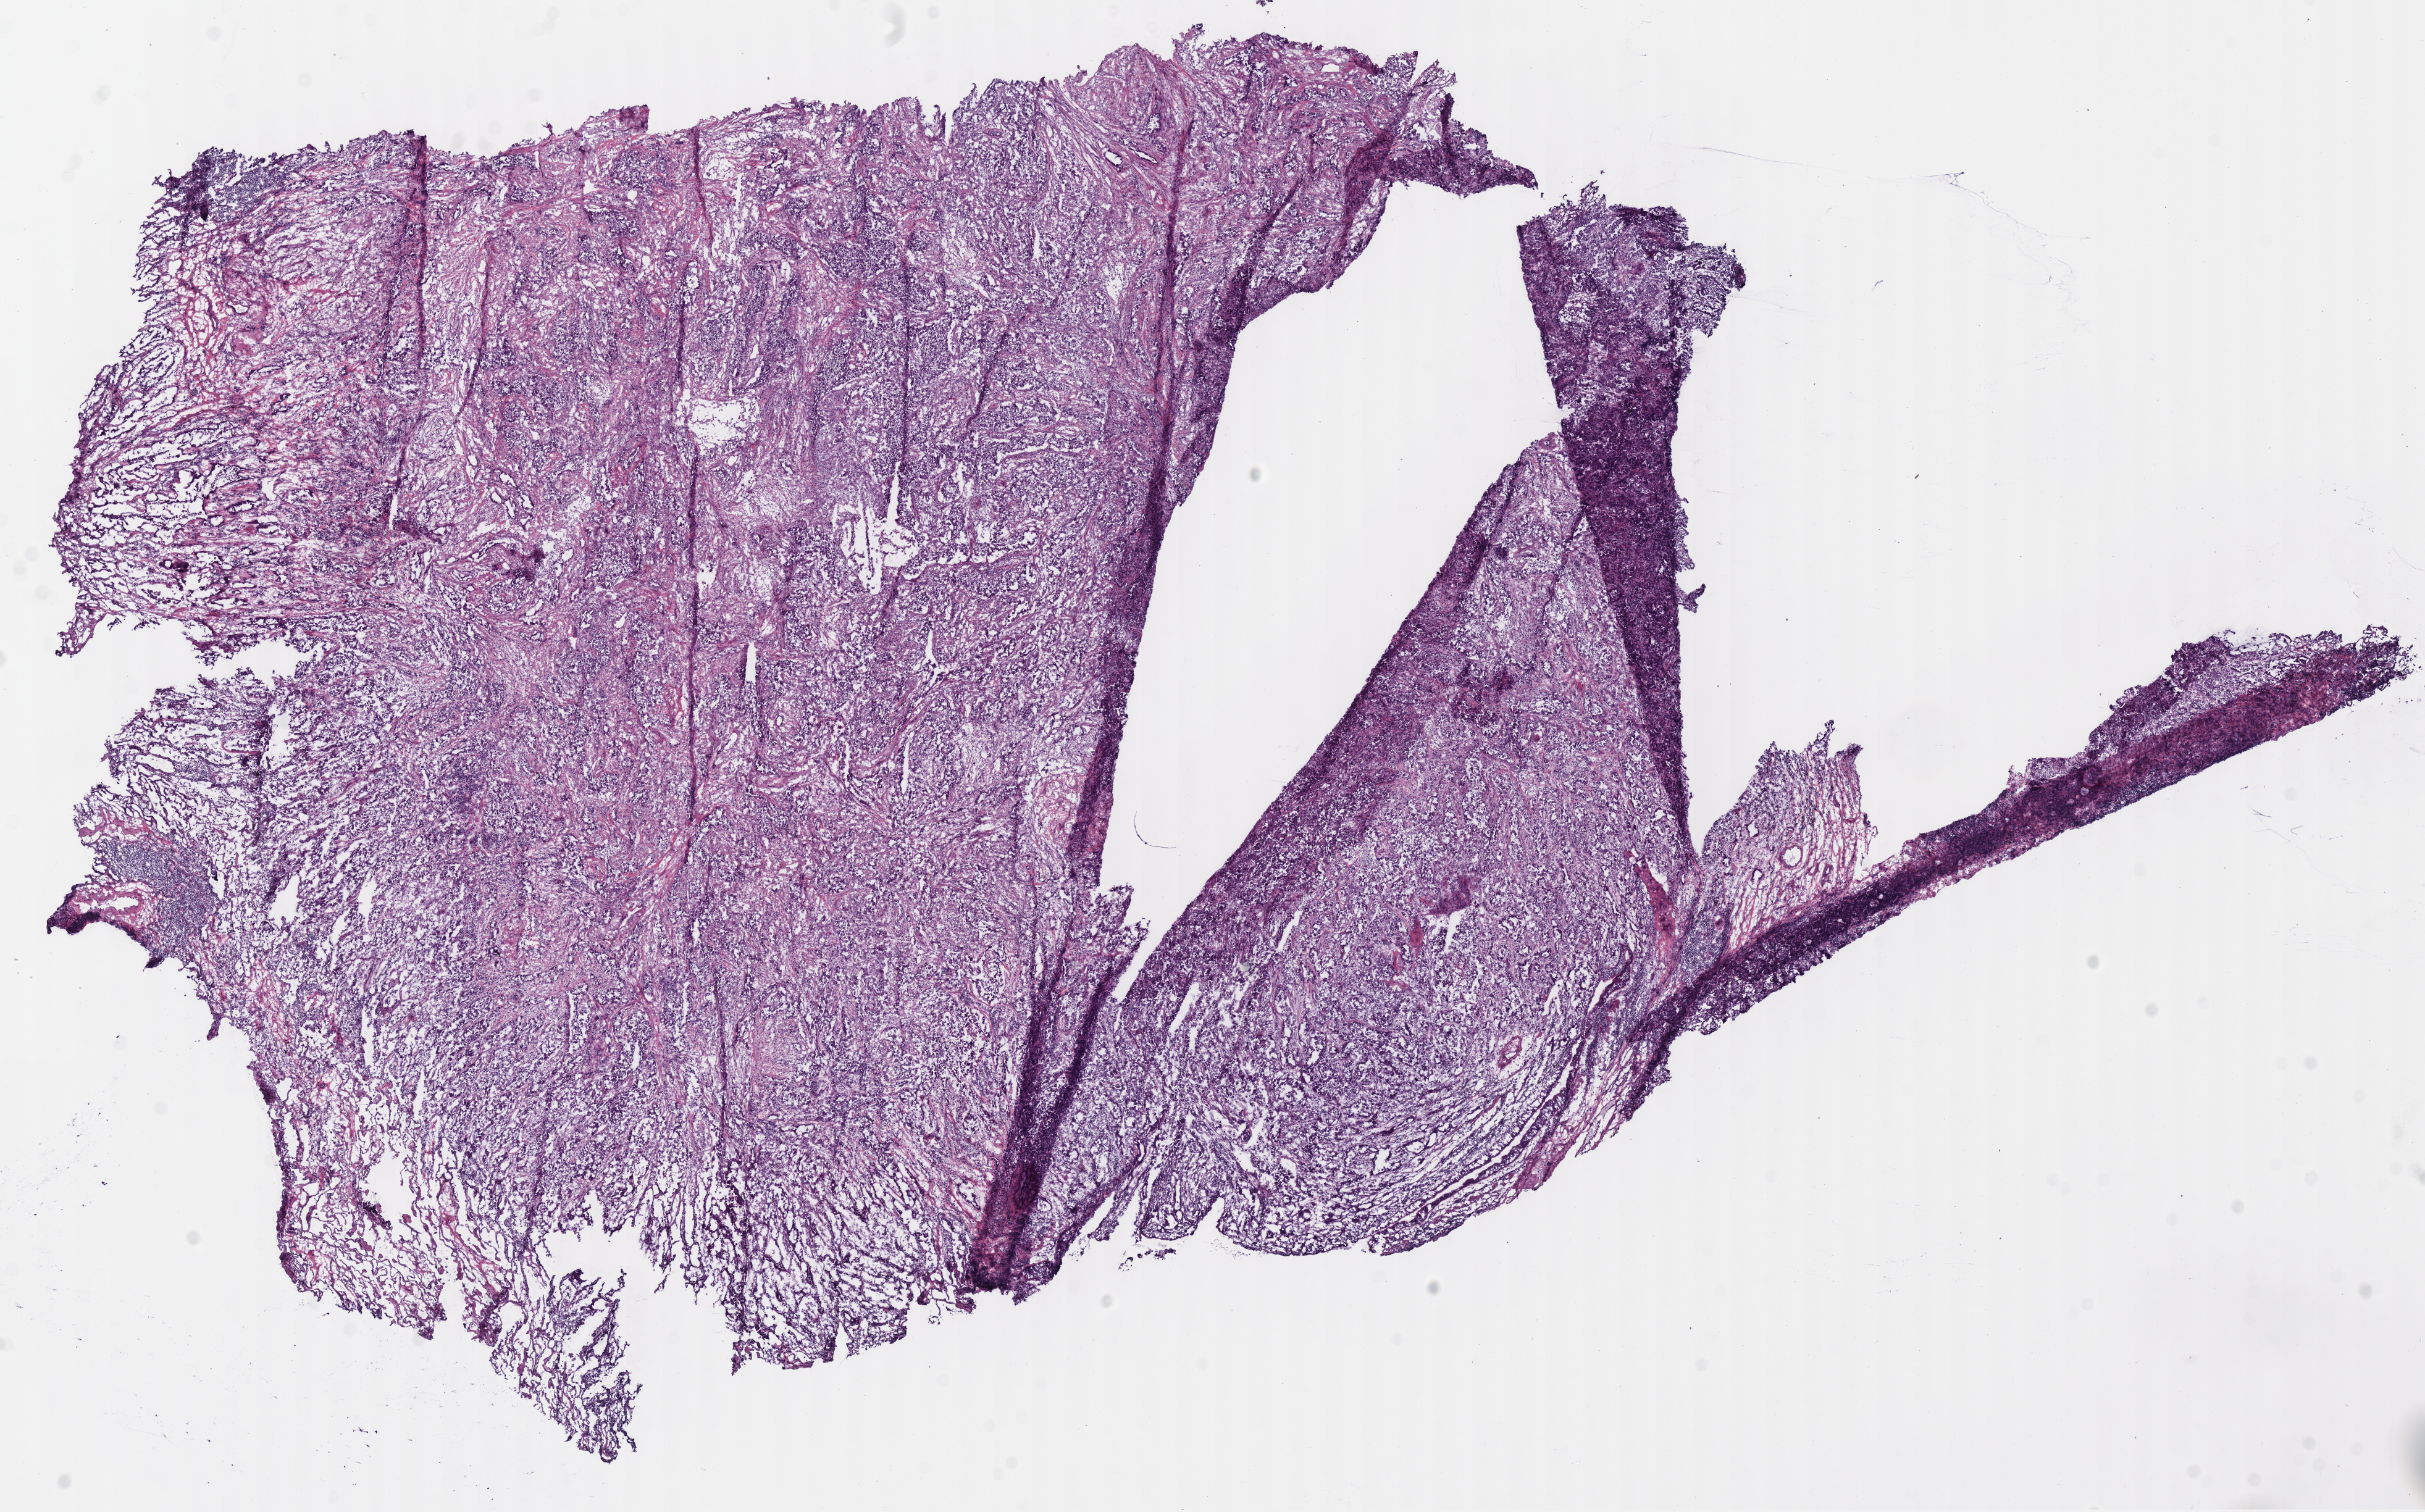
Digitized Hematoxylin and eosin (H&E) stained tissue section (whole slide), shown as a low-resolution overview of the whole scanned area (about 15.5 x 9.6 mm, from a 40x scan). Frozen section from the bottom of the tissue portion. Lung, primary tumour sample. Female patient; age at initial diagnosis 66 years.
Diagnosis: Adenocarcinoma, NOS (upper lobe, lung).